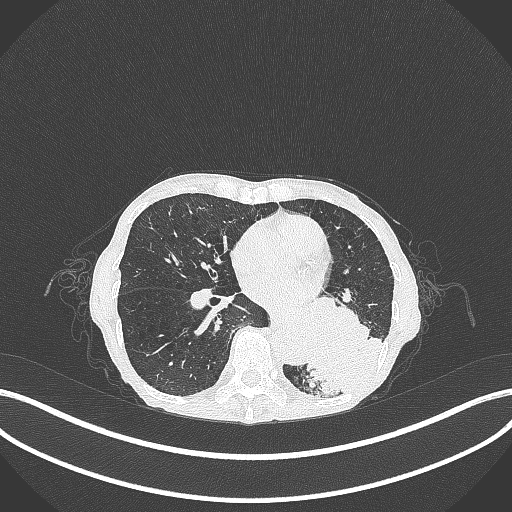
Chest CT, one axial slice. Position 118 of 347 along the scan axis. 120 kVp. Lung window (W 1500 / L -600 HU). 1 mm slice thickness. 512 × 512 image matrix. Patient: female, 70 years. Case-level facts recorded for this patient, not image findings: clinical TNM (as recorded): T3 N0 M0; histopathological grade: G3.
Annotated regions visible in this slice (bounding box drawn by a radiologist):
- lung tumour (recorded histology: small cell carcinoma): bounding box <294,307,385,398> (left, top, right, bottom; pixels)